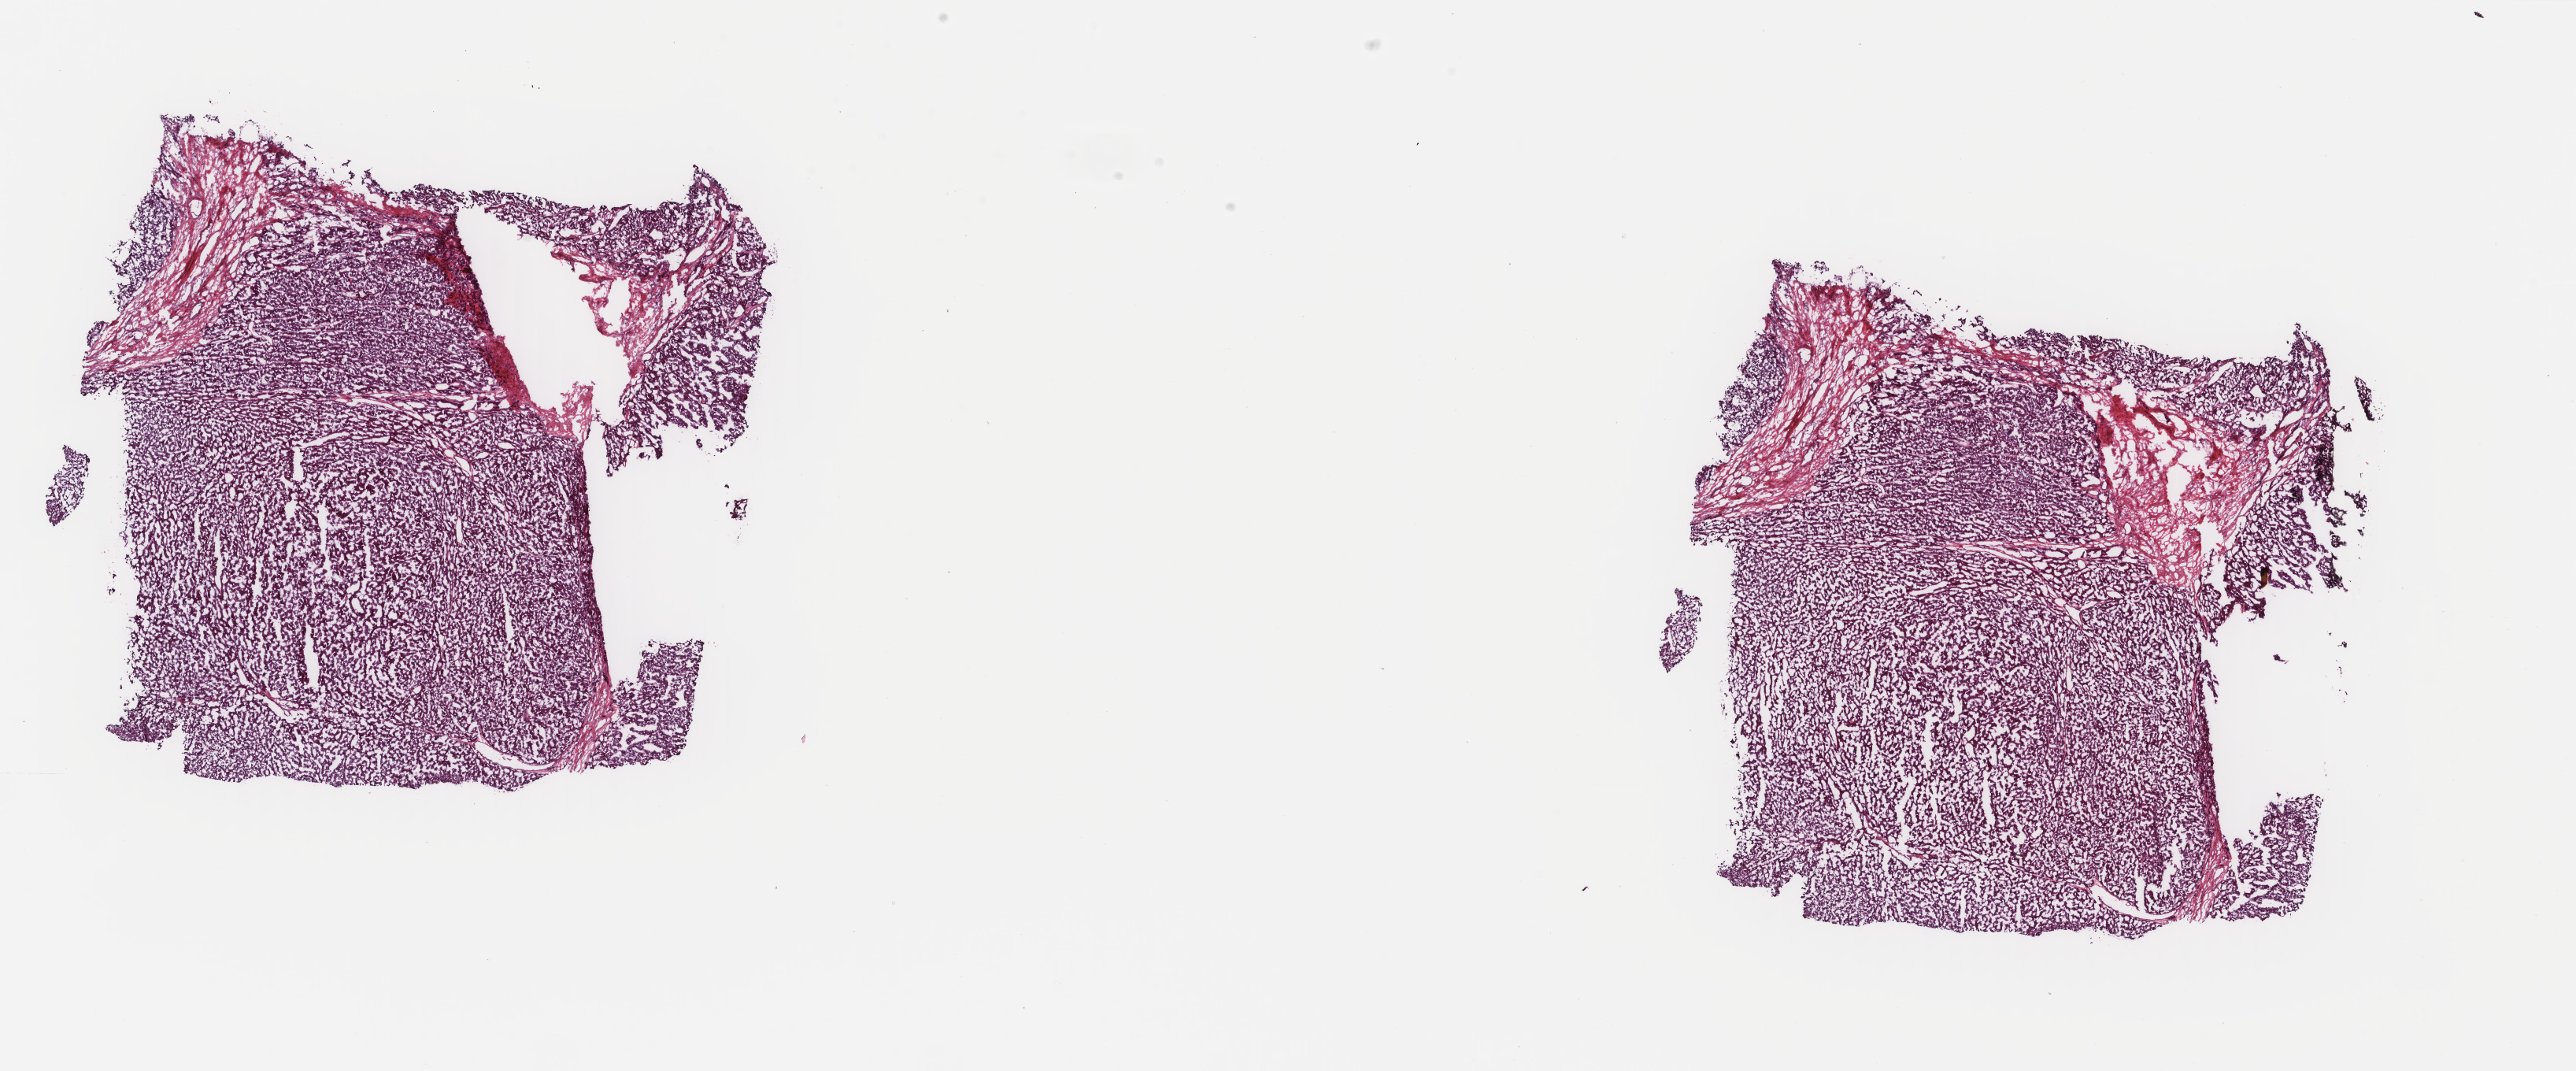
H&E-stained whole-slide image, whole scanned area (about 26.0 x 10.8 mm) shown as a low-resolution overview. Frozen section from the top of the tissue portion. Sample: primary tumour, liver. Female patient; age at initial diagnosis 66 years. Histologic grade: G2 (moderately differentiated). Pathologist review of this section (percent, as recorded): tumour cells 90%, tumour nuclei 95%, normal cells 0%, stromal cells 10%, necrosis 0%. Infiltration values recorded for this section: lymphocyte infiltration 0%, monocyte infiltration 0%, neutrophil infiltration 0%.
TNM: T3 N0 M0. AJCC pathologic stage: III. Pathologic diagnosis: Hepatocellular carcinoma, NOS.